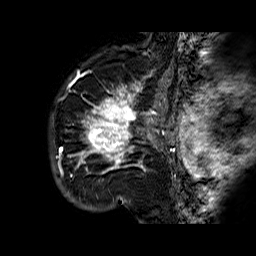
Breast MRI (dynamic contrast-enhanced), one sagittal slice. Slice 50 of 60 in the series (ordered by position). Dynamic contrast-enhanced series, time point 2 of 6 at this slice position (early post-contrast). 1.5 T. TE 6.3 ms, TR 32.4 ms. 4 mm slice thickness. 256 × 256 image matrix, field of view 200 × 200 mm. Female patient. Case-level facts recorded for this patient, not image findings: setting: breast cancer imaged before/during neoadjuvant chemotherapy; receptor status: HR-positive, HER2-negative.
Annotated regions visible in this slice (semi-automatic segmentation, software-assisted and operator-edited):
- analysis volume of interest (the breast-tissue region the enhancement analysis was run in; not a lesion): bounding box <68,72,177,183> (left, top, right, bottom; pixels)
- tumour enhancement mask (voxels above the 100 % enhancement threshold inside the analysis volume of interest): <73,72,175,174>